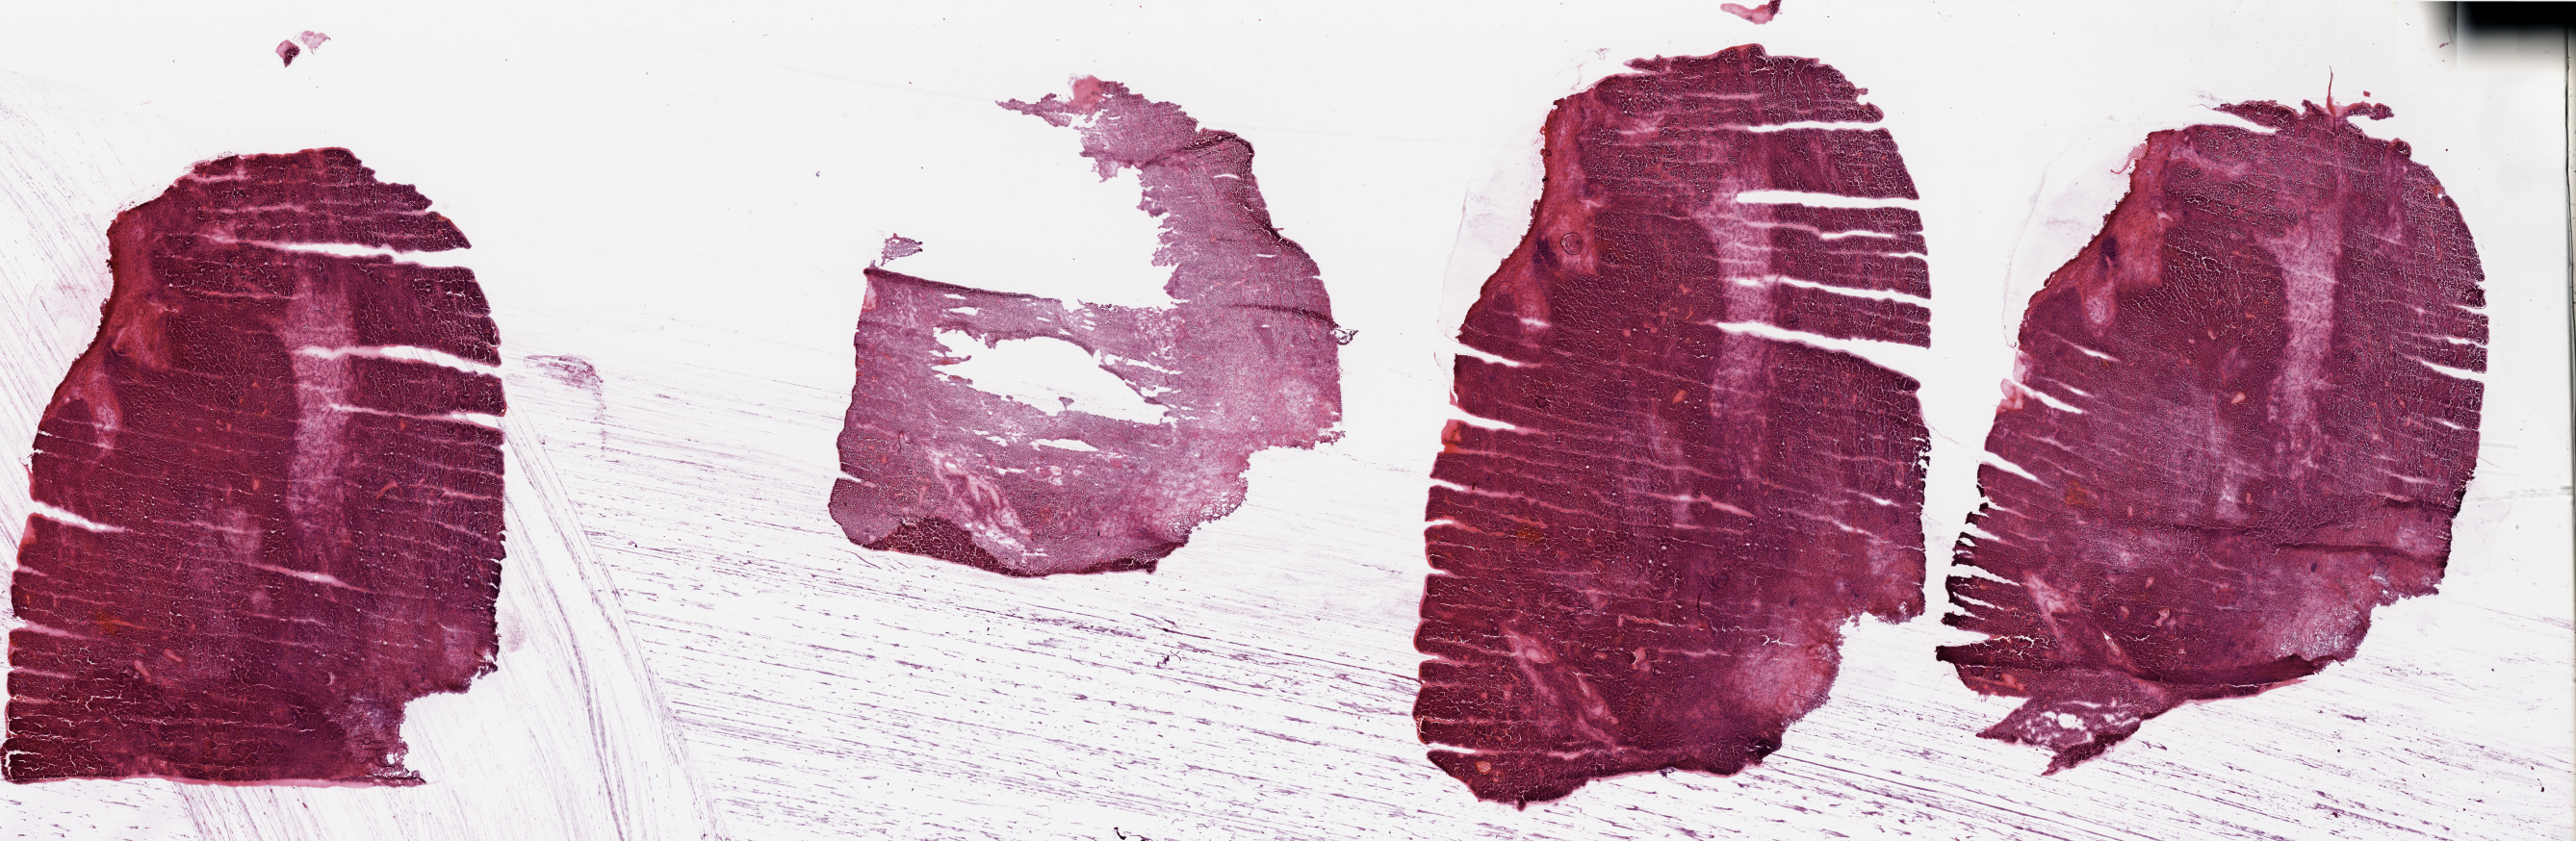
Whole-slide histology image, H&E — low-resolution overview of the scanned area, about 42.3 x 13.8 mm; tumour tissue sample, sampled site: kidney. 68-year-old male patient. Histologic grade: G3 (poorly differentiated). Pathologist review of this section (percent, as recorded): tumour nuclei 80%, necrosis 5%.
Histologic diagnosis: Renal cell carcinoma, NOS. Primary tumour site (as recorded): lower pole. AJCC pathologic stage: III.